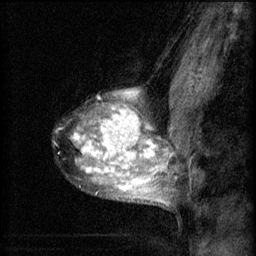
Breast MRI (dynamic contrast-enhanced), one sagittal slice. Position 45 of 60 along the scan axis. 3 images stored at this slice position (order not interpretable as contrast timing). 1.5 T. TE 4.2 ms, TR 8.2 ms. 2 mm slice thickness. 256 × 256 image matrix, field of view 180 × 180 mm. Patient: female, 40 years.
Structures marked on this image (semi-automatically segmented with operator editing):
- analysis volume of interest (the breast-tissue region the enhancement analysis was run in; not a lesion): bounding box [x1, y1, x2, y2] px = [65, 82, 167, 207]
- tumour enhancement mask (voxels above the 70 % enhancement threshold inside the analysis volume of interest): [75, 90, 167, 201]